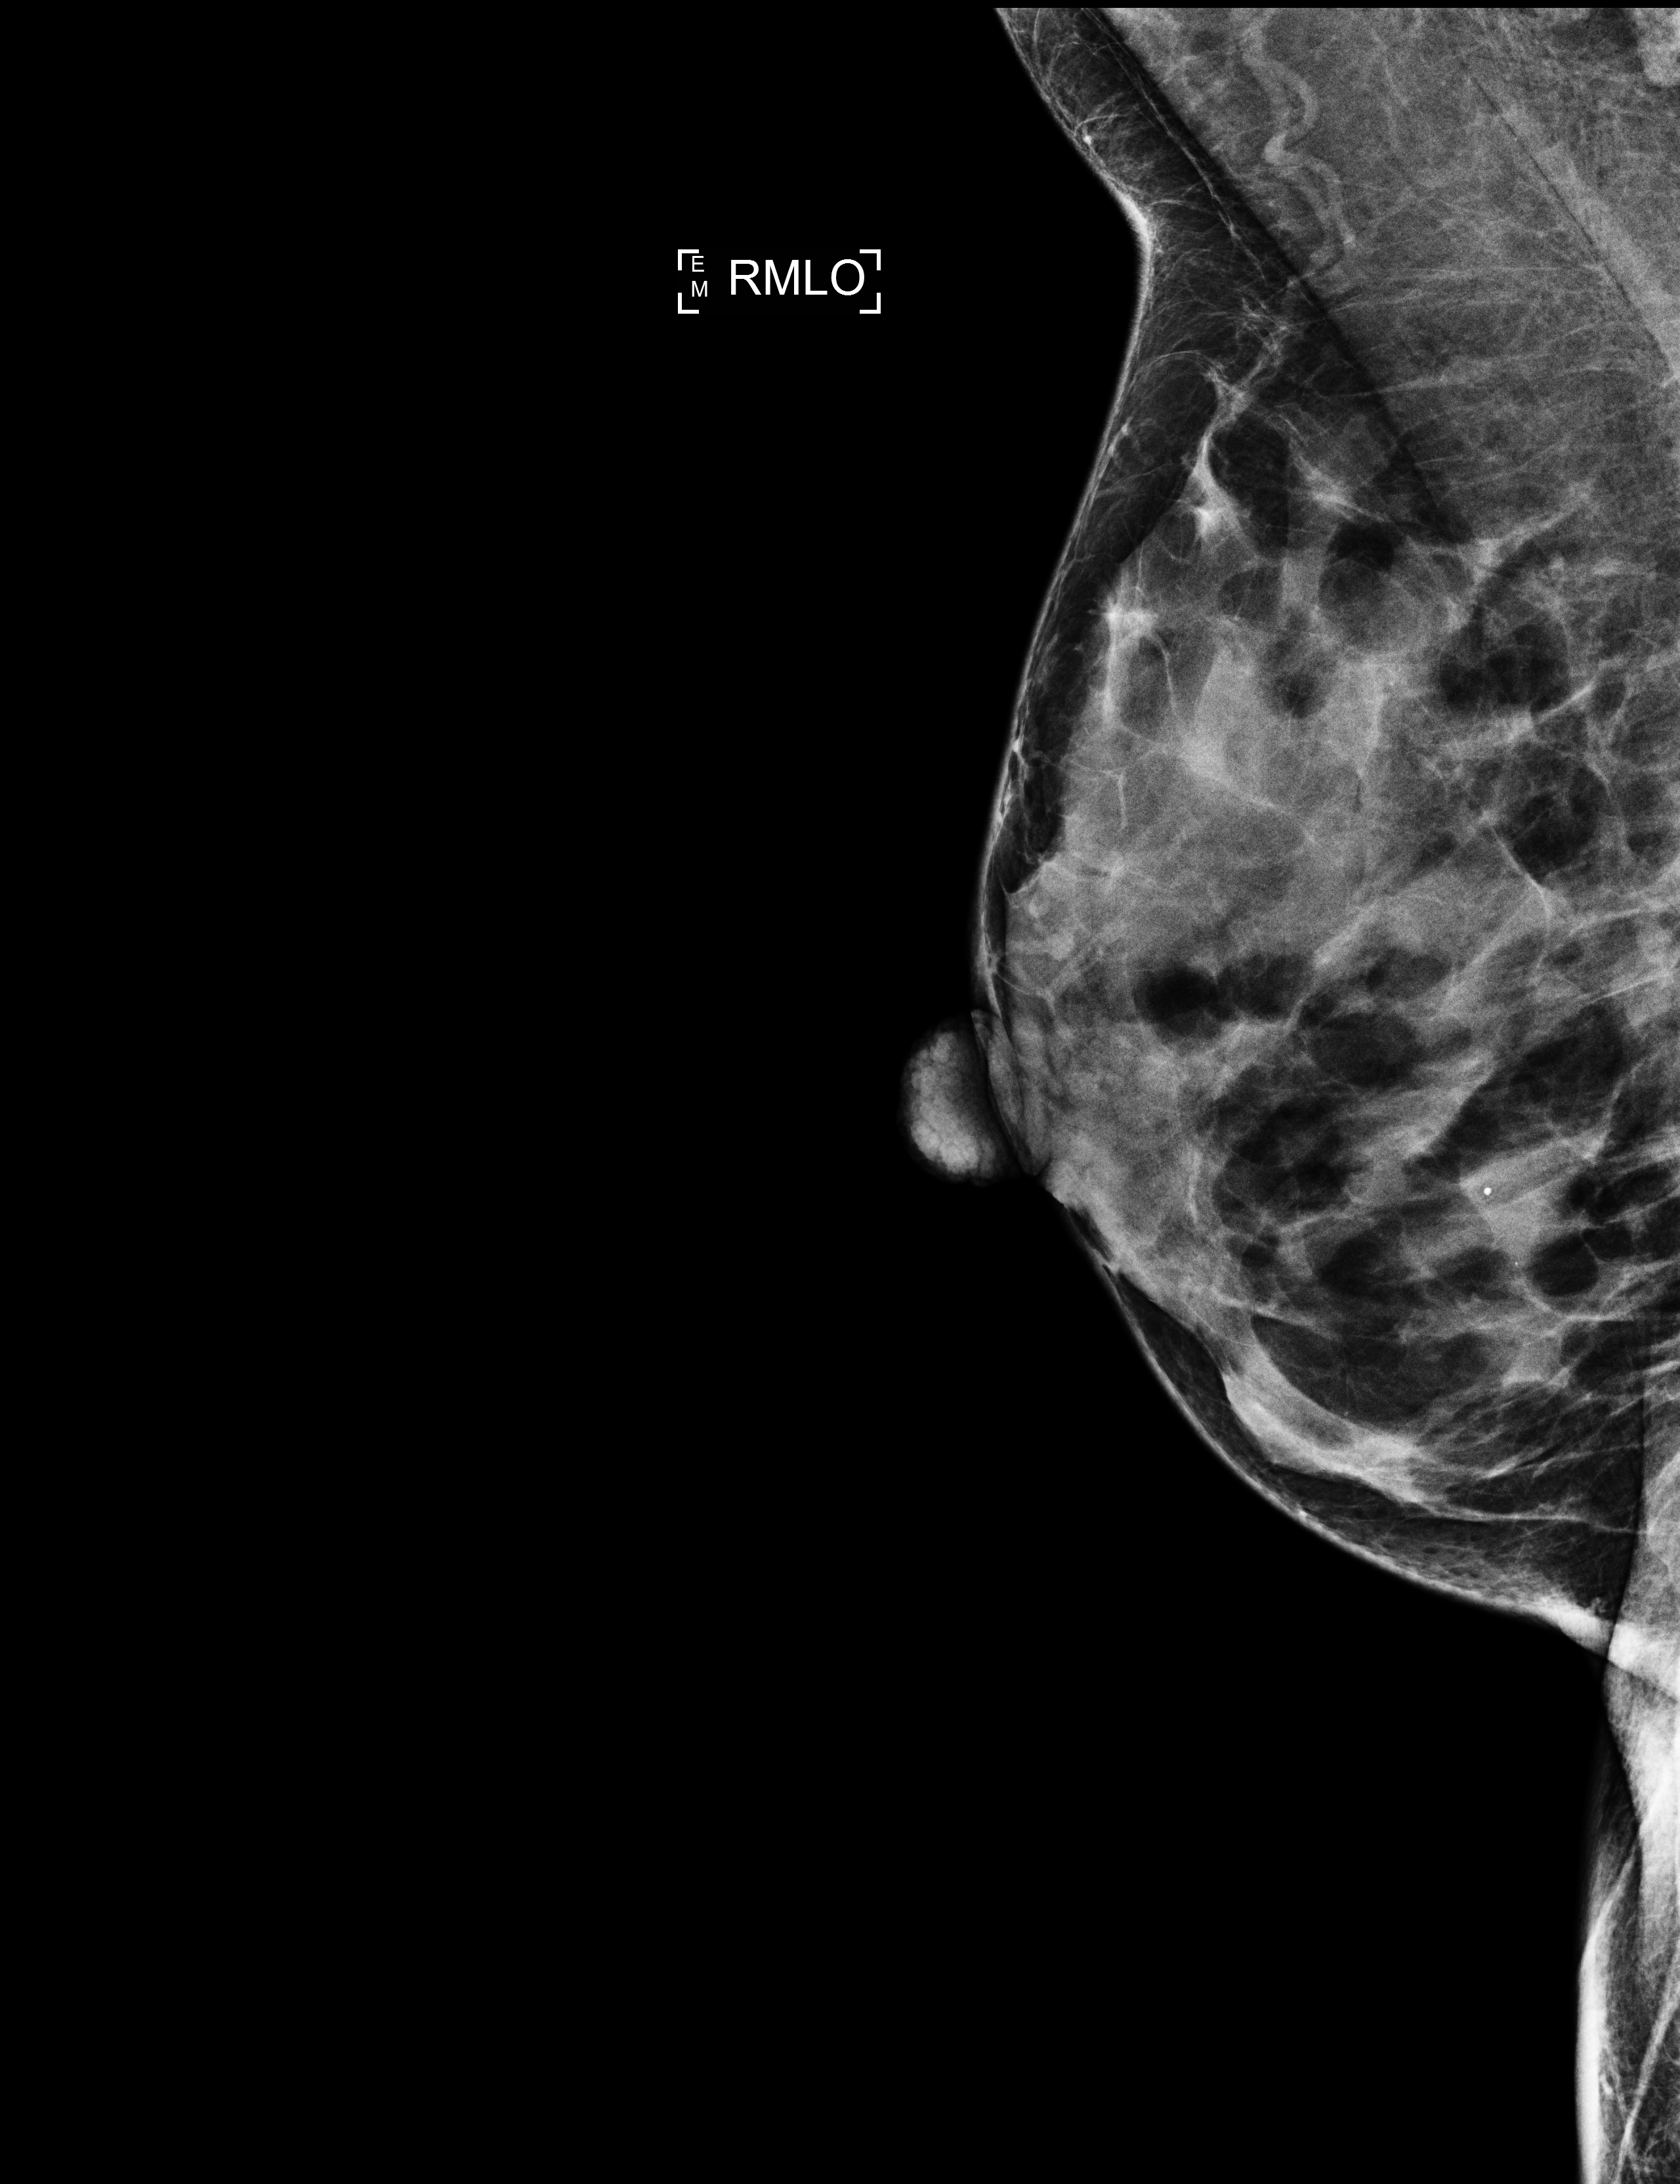
Screening examination, system: Selenia Dimensions. Female patient, age 43 years.
Image type: full-field digital mammogram. Breast: right. Projection: mediolateral oblique (MLO) view.